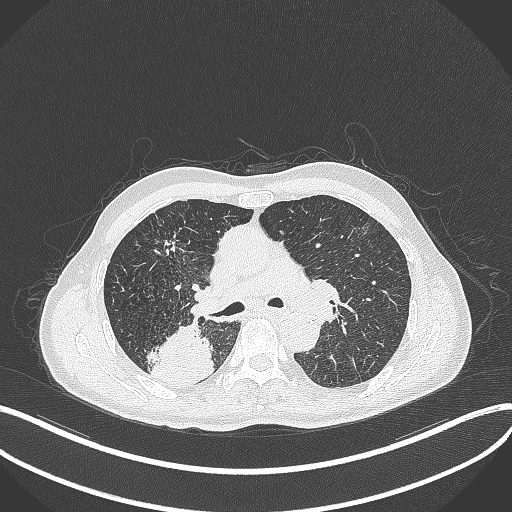
Chest CT, one axial slice. Reconstruction kernel B70f. Lung window (W 1500 / L -600 HU). 512 × 512 image matrix, field of view 400 × 400 mm. Male patient, age 79 years. From the clinical record (not read from this slice): clinical TNM (as recorded): T3 N0 M0.
Outlined on this slice (bounding box drawn by a radiologist):
- lung tumour (recorded histology: adenocarcinoma): bounding box <146,318,214,388> (left, top, right, bottom; pixels)